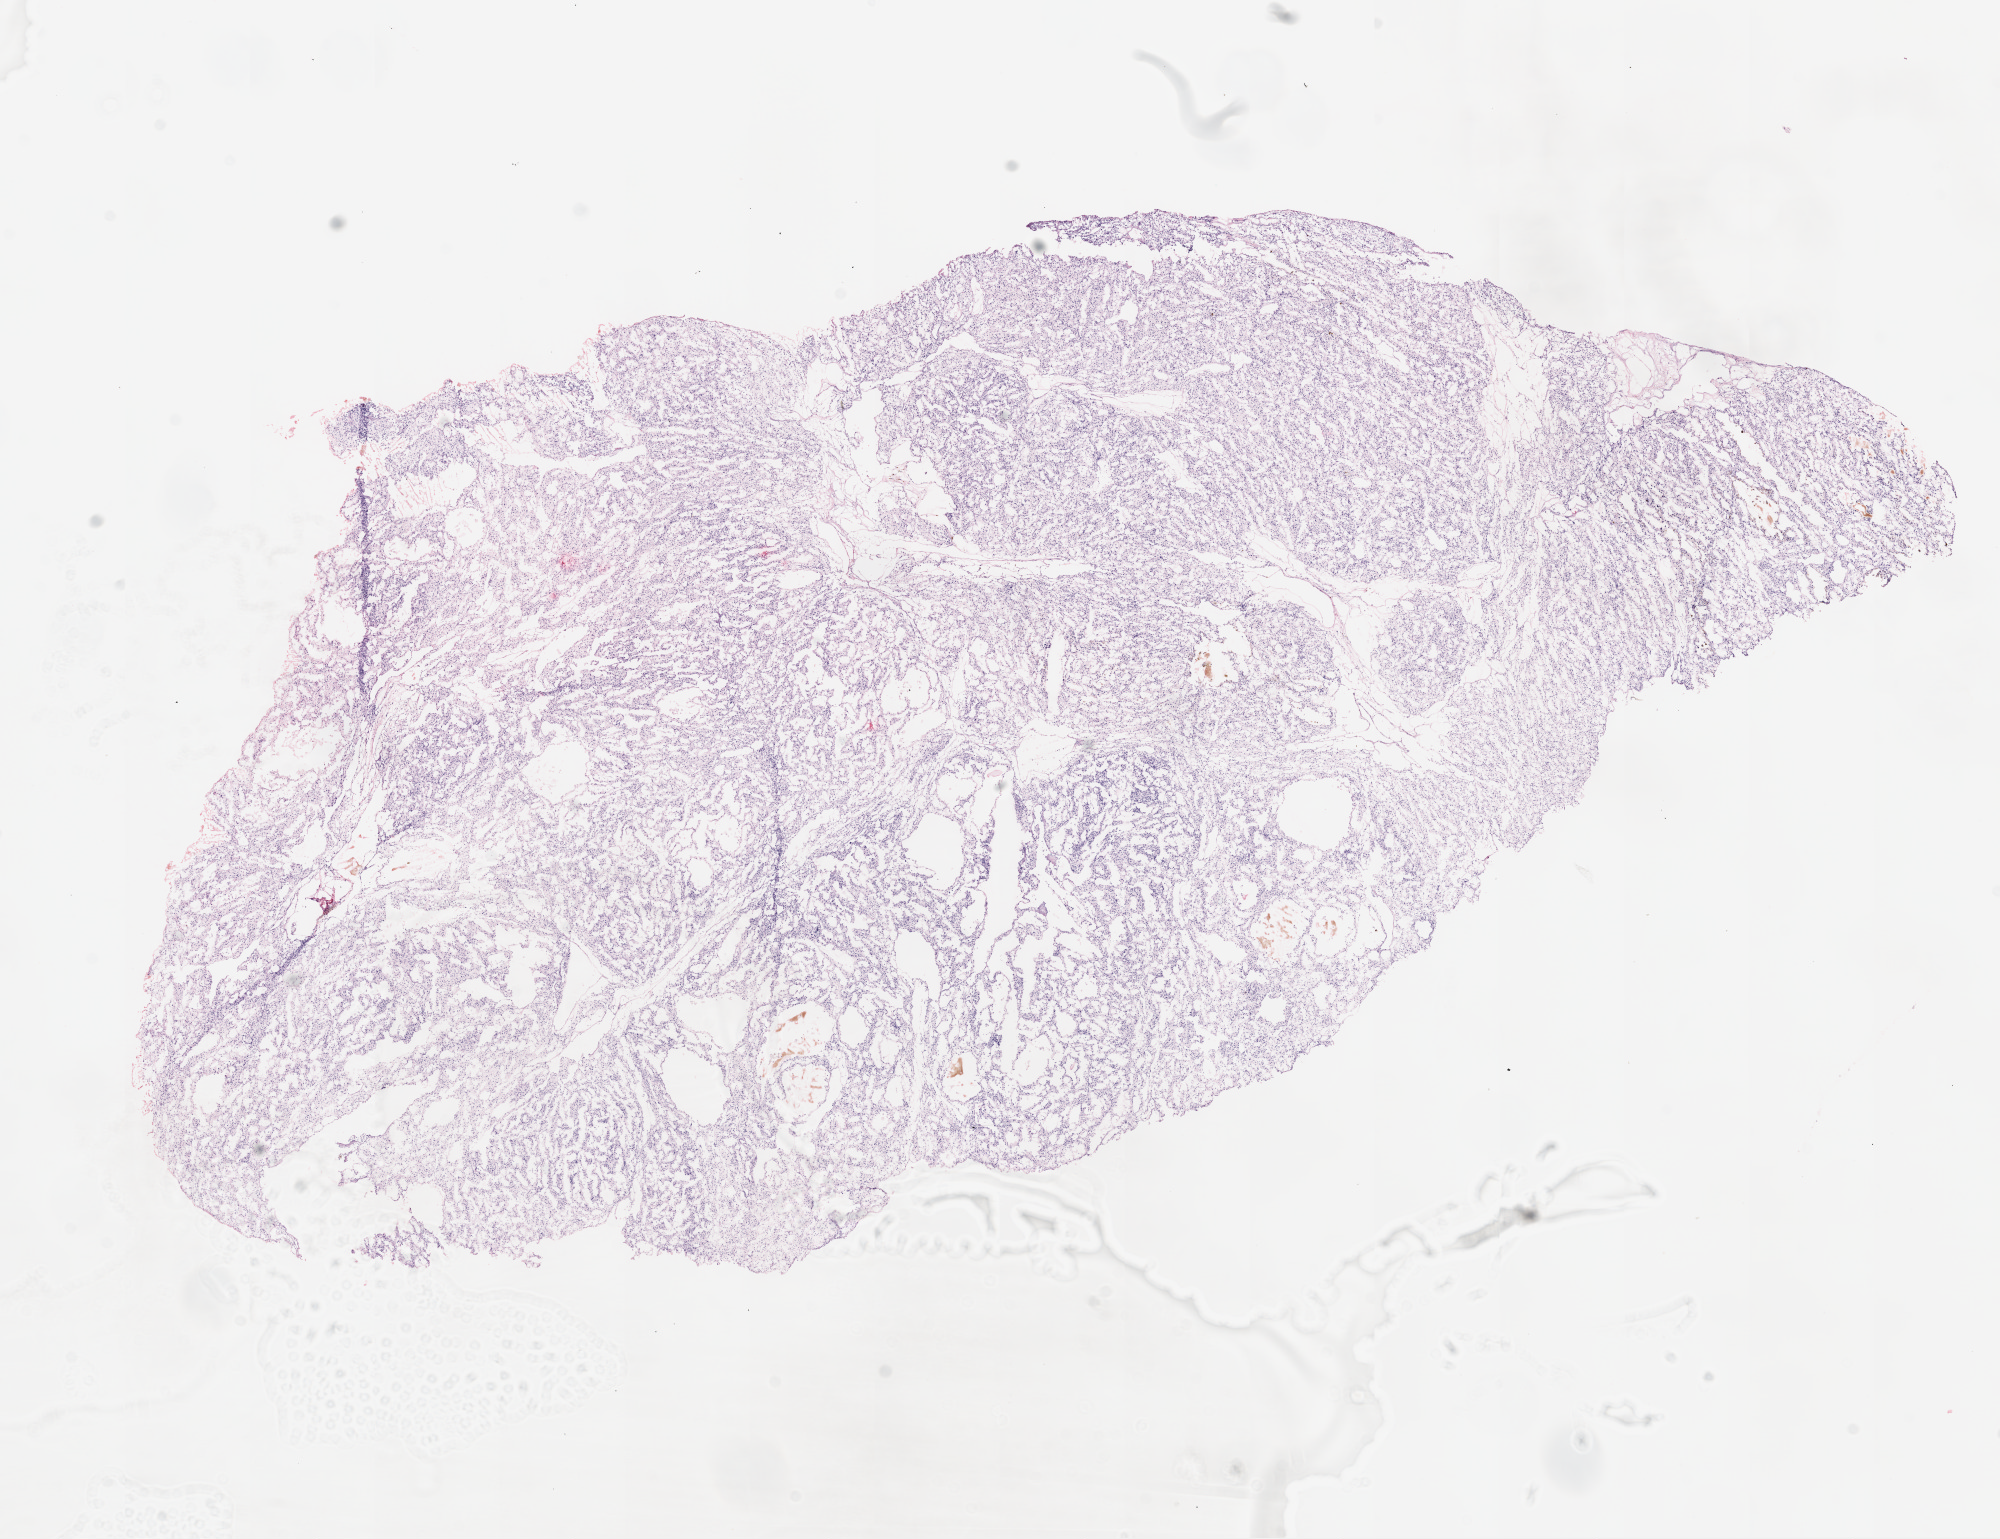
Whole-slide histology image, H&E, low-resolution overview of the scanned area, about 16.0 x 12.3 mm. Frozen section. Primary tumour sample from the kidney. Patient: male, age at initial diagnosis 67 years. Histologic grade: G2 (moderately differentiated). Slide review estimates, as recorded: tumour cells 95%, tumour nuclei 90%, normal cells 0%, stromal cells 5%, necrosis 0%. Infiltration values recorded for this section: lymphocyte infiltration 2%, monocyte infiltration 0%, neutrophil infiltration 0%.
Histologic diagnosis: Clear cell adenocarcinoma, NOS. AJCC pathologic stage: II.